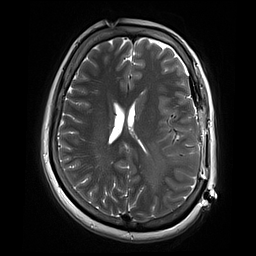
Brain MRI from a brain-tumour surgery series, one axial slice; position 31 of 70 along the scan axis; 2 mm slice thickness; 256 × 256 image matrix. Case-level facts recorded for this patient, not image findings: histopathology: Glioblastoma; WHO grade: 4; IDH mutation: no.
Annotated regions visible in this slice (outlined manually by an expert reader):
- residual tumour: bounding box <158,115,173,131> (left, top, right, bottom; pixels)